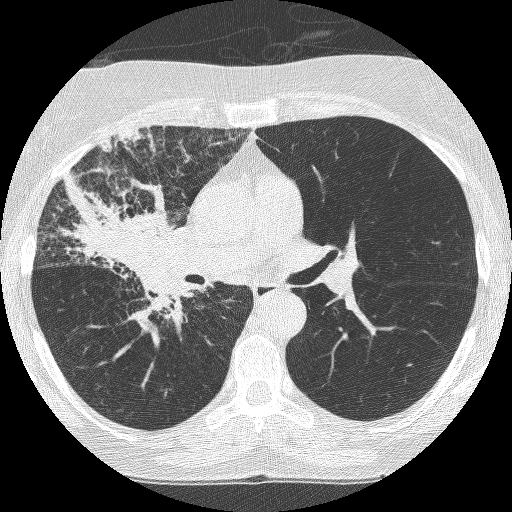
Chest CT (low-dose screening protocol), one axial image, third screening round (two years after baseline), lung window (W 1500 / L -600 HU), slice 148 of 253 in the series. Female participant, aged 64 years at enrolment. Former smoker at enrolment.
- Lesion marked by an expert reader, bounding box <68,183,202,318> (left, top, right, bottom; pixels).
- Reader record for this screening exam (exam-level; its link to the box is not recorded): non-calcified nodule or mass ≥4 mm, right upper lobe, 49 × 43 mm, spiculated (stellate) margins, soft tissue attenuation, pre-existing on the prior screen: yes; interval growth: yes.